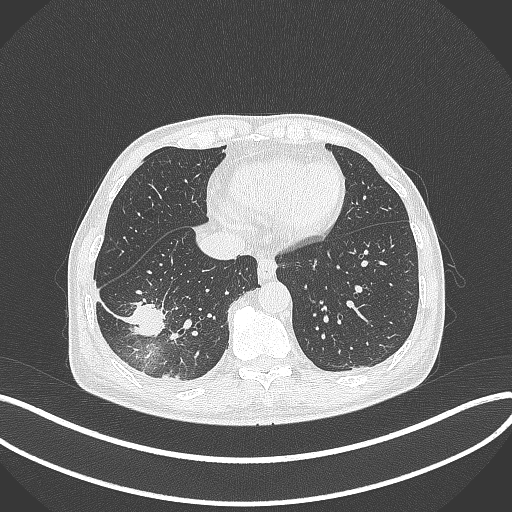
Chest CT, one axial slice; position 104 of 388 along the scan axis; reconstruction kernel B70f; lung window (W 1500 / L -600 HU); 1 mm slice thickness; 512 × 512 image matrix. Patient: male, 64 years. From the clinical record (not read from this slice): clinical TNM (as recorded): T3 N0 M0; histopathological grade: G2-3.
Annotated regions visible in this slice (rectangle marked by the reading radiologist):
- lung tumour (recorded histology: adenocarcinoma): bounding box [x1, y1, x2, y2] px = [123, 300, 170, 339]